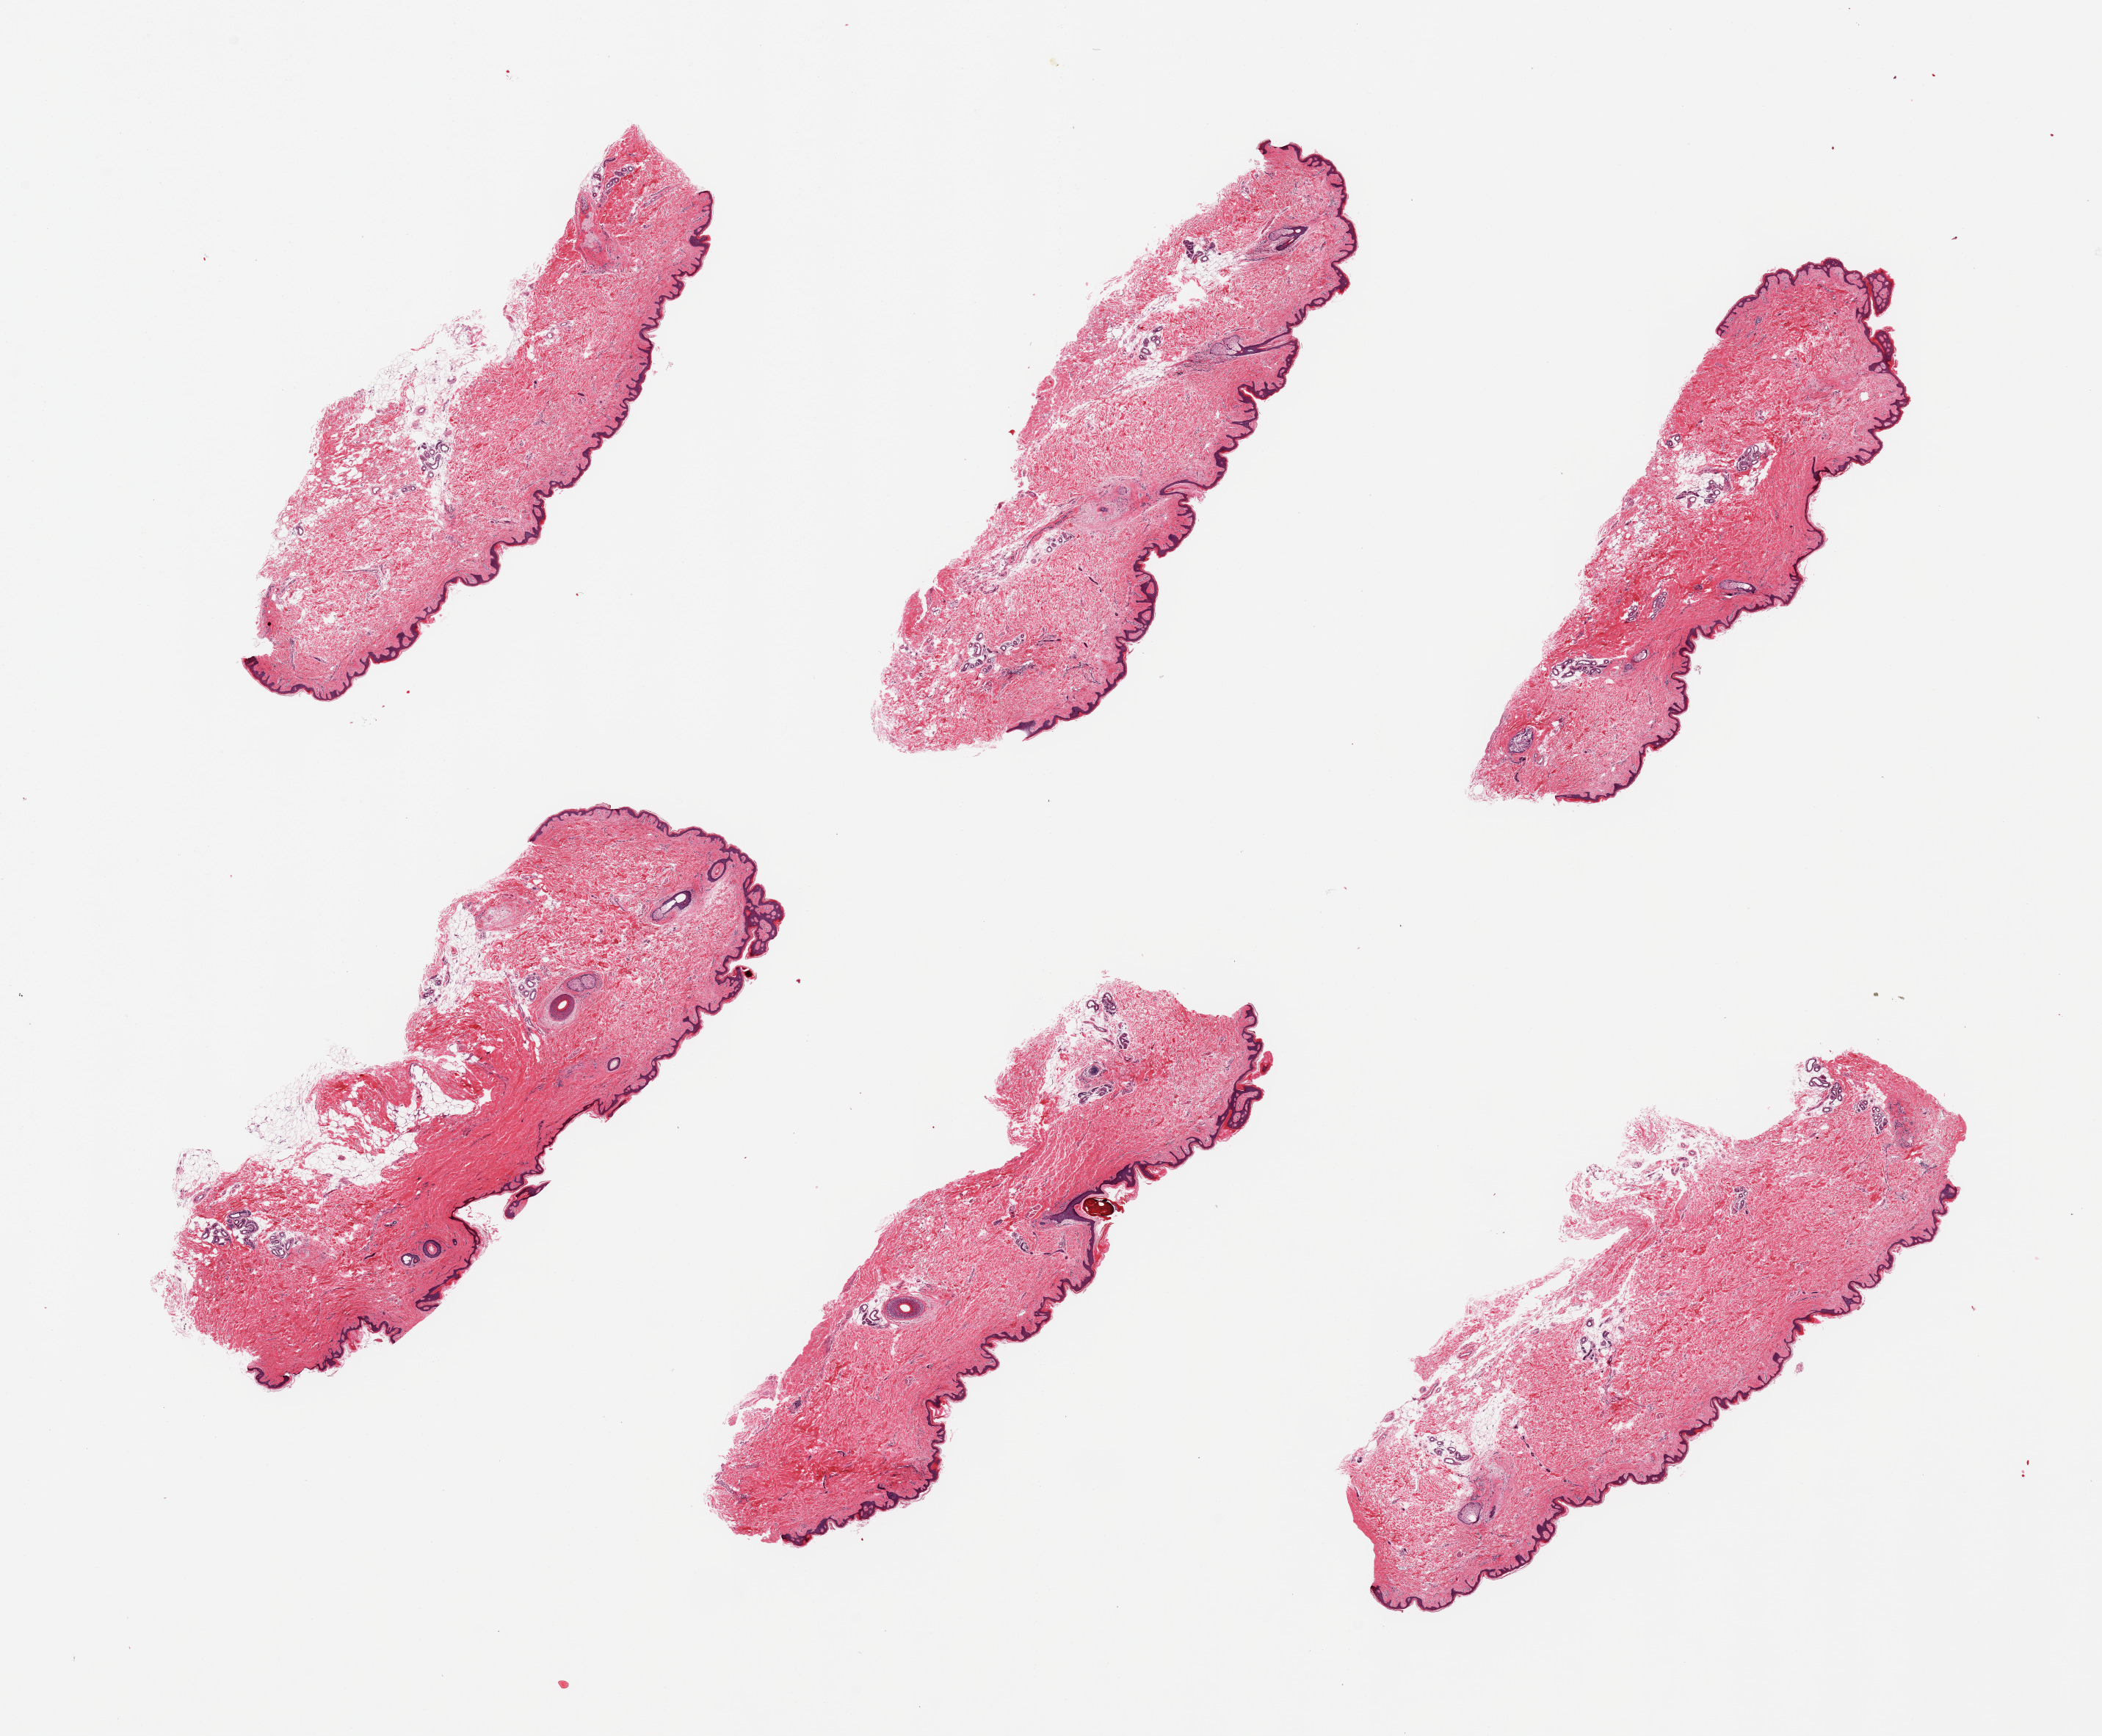
Hematoxylin and eosin (H&E) whole-slide image, whole scanned area (about 22.6 x 18.7 mm) shown as a low-resolution overview. PAXgene-fixed paraffin-embedded (PFPE) section. Sampled site (target tissue): skin of suprapubic region. Tissue donor sample. Donor: female.
* review note (as recorded): 6 pieces; well trimmed; 10% intradermal fat